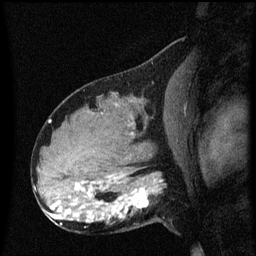
Breast MRI (dynamic contrast-enhanced), one sagittal slice. Slice 32 of 60 in the series (ordered by position). Dynamic contrast-enhanced series, image 2 of 3 at this slice position (ordered by acquisition). 1.5 T. TE 4.2 ms, TR 8.4 ms. 256 × 256 image matrix. Female patient, age 31 years. Case-level facts recorded for this patient, not image findings: setting: breast cancer imaged before/during neoadjuvant chemotherapy; receptor status: HR-positive, HER2-negative.
Outlined on this slice (semi-automatic segmentation, software-assisted and operator-edited):
- analysis volume of interest (the breast-tissue region the enhancement analysis was run in; not a lesion): box from (x=102, y=166) to (x=169, y=229) px
- tumour enhancement mask (voxels above the 70 % enhancement threshold inside the analysis volume of interest): (x=113, y=188)–(x=154, y=219)